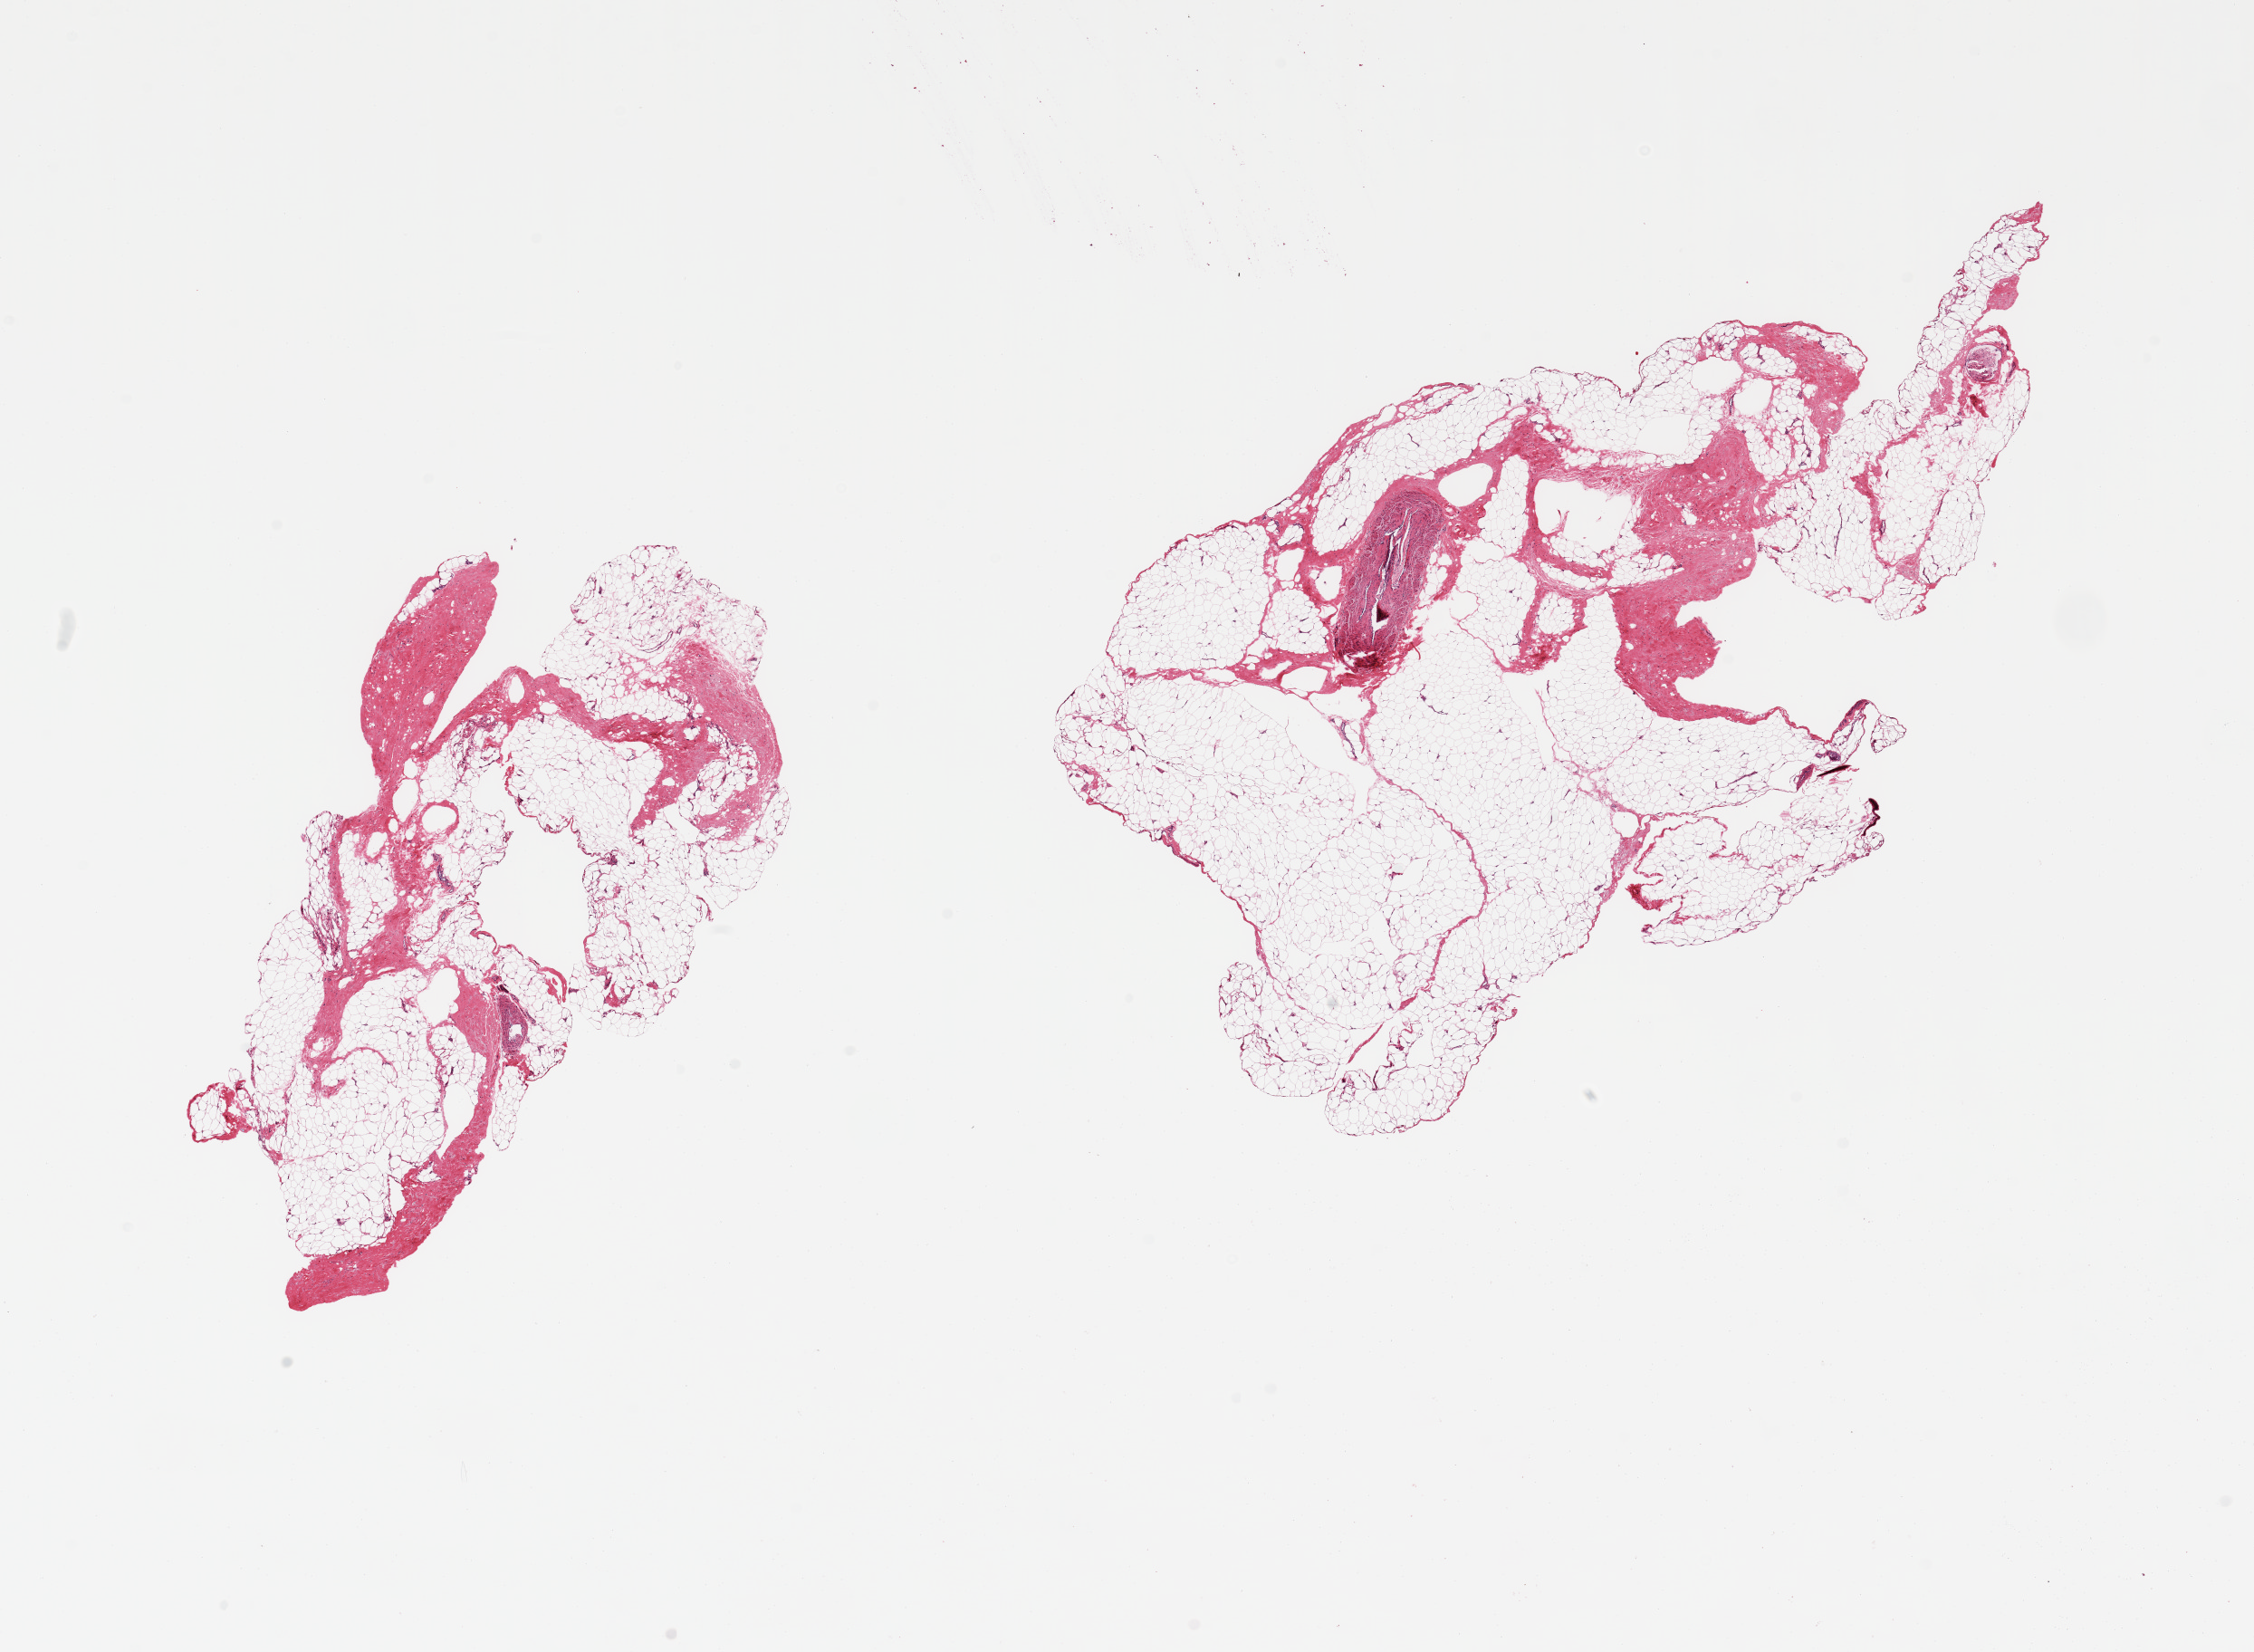
Haematoxylin and eosin whole-slide image — low-resolution overview of the scanned area, about 19.7 x 14.4 mm. PAXgene-fixed, paraffin-embedded tissue. Target tissue: adipose tissue. Tissue donor sample. Donor sex: male.
Review note (as recorded): 2 pieces, ~30% fascia/vascular elements.